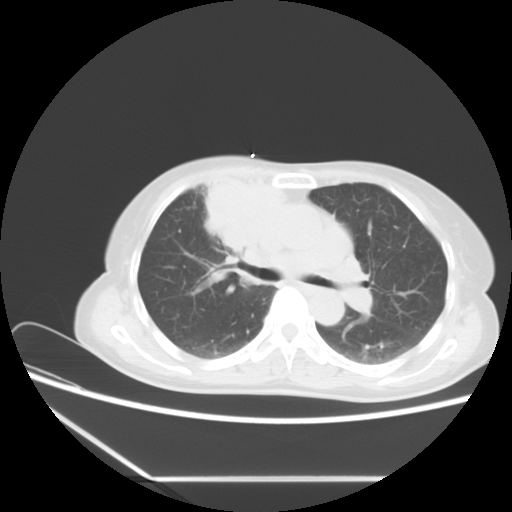
Chest CT, one axial slice; reconstruction kernel STANDARD; 120 kVp; lung window (W 1500 / L -600 HU); 5 mm slice thickness; 512 × 512 image matrix, field of view 350 × 350 mm. Female patient, age 63 years. From the clinical record (not read from this slice): clinical TNM (as recorded): T2b N1 M0.
Outlined on this slice (rectangle marked by the reading radiologist):
- lung tumour (recorded histology: adenocarcinoma): bounding box (x1, y1, x2, y2) in pixels: (198, 171, 290, 251)